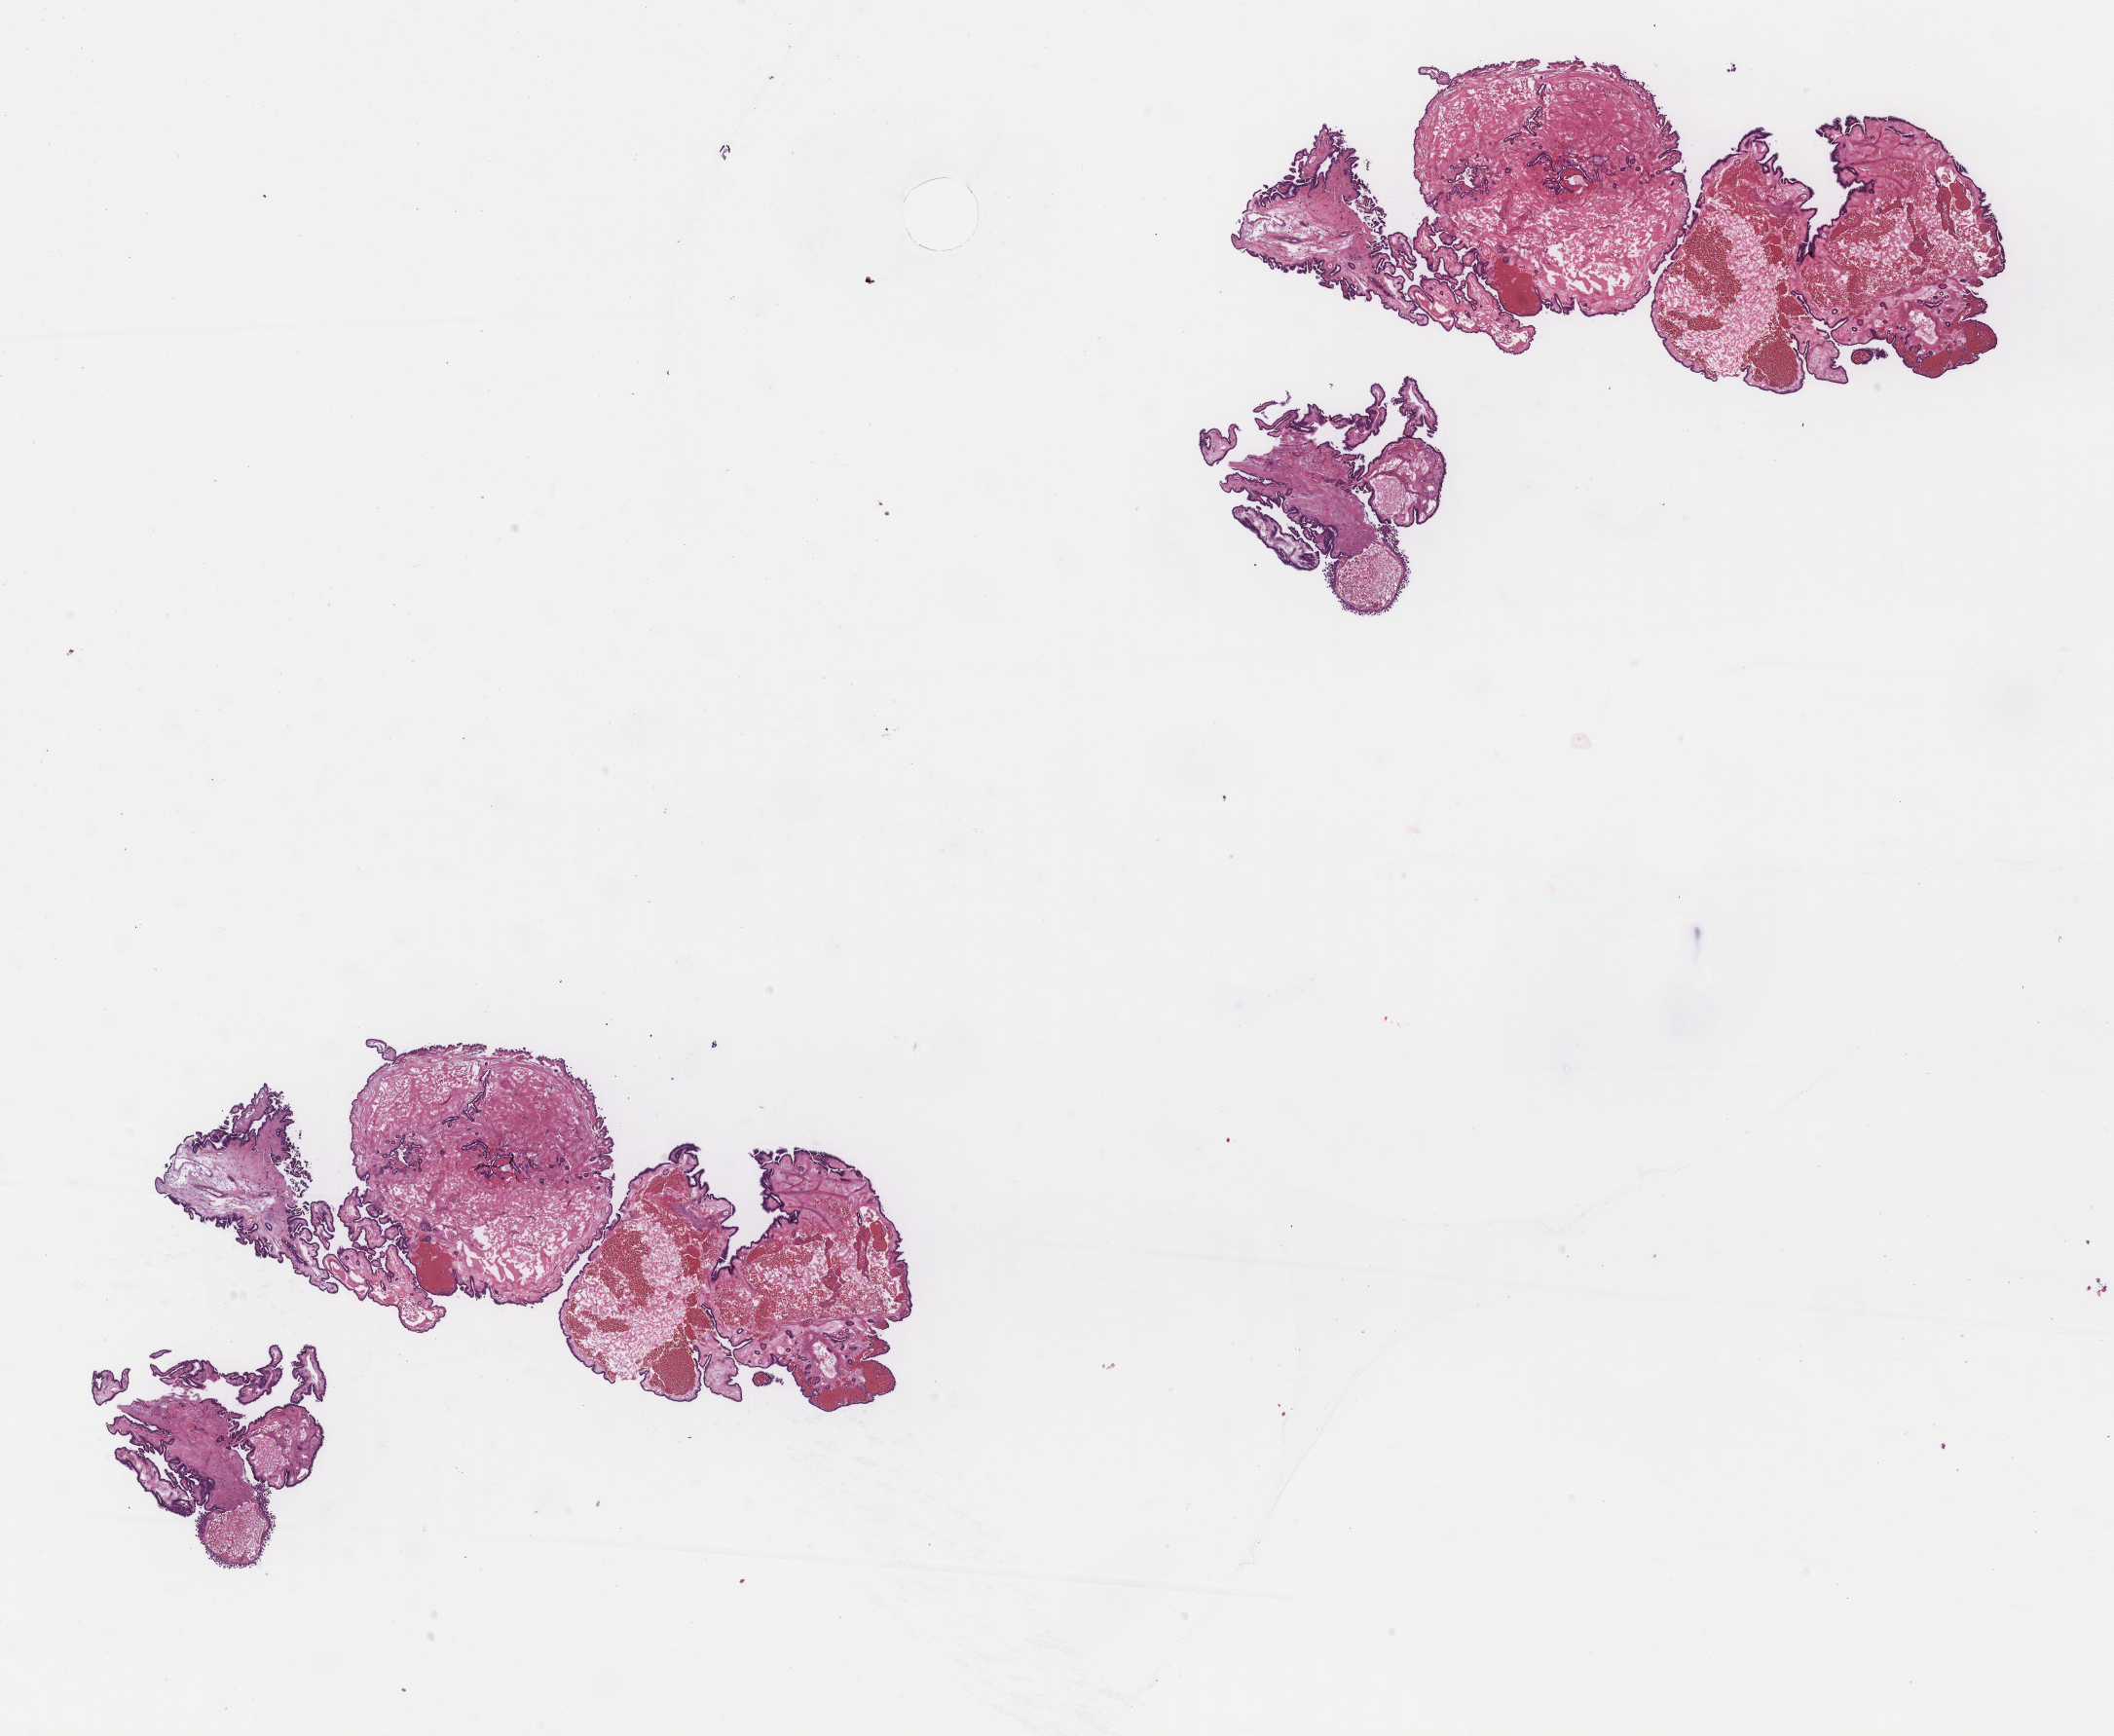
Digitized H&E-stained tissue section (whole slide), shown as a low-resolution overview of the whole scanned area (about 17.2 x 14.2 mm, slide scanned at 40x), formalin-fixed paraffin-embedded (FFPE) diagnostic section, primary tumour sample from the thyroid. Female, age 40 years at initial diagnosis.
AJCC pathologic stage: I (7th edition). TNM: T2 N0 MX. Diagnosis: Papillary adenocarcinoma, NOS (thyroid gland). Lymph nodes positive (case pathology): 0 of 3 examined.